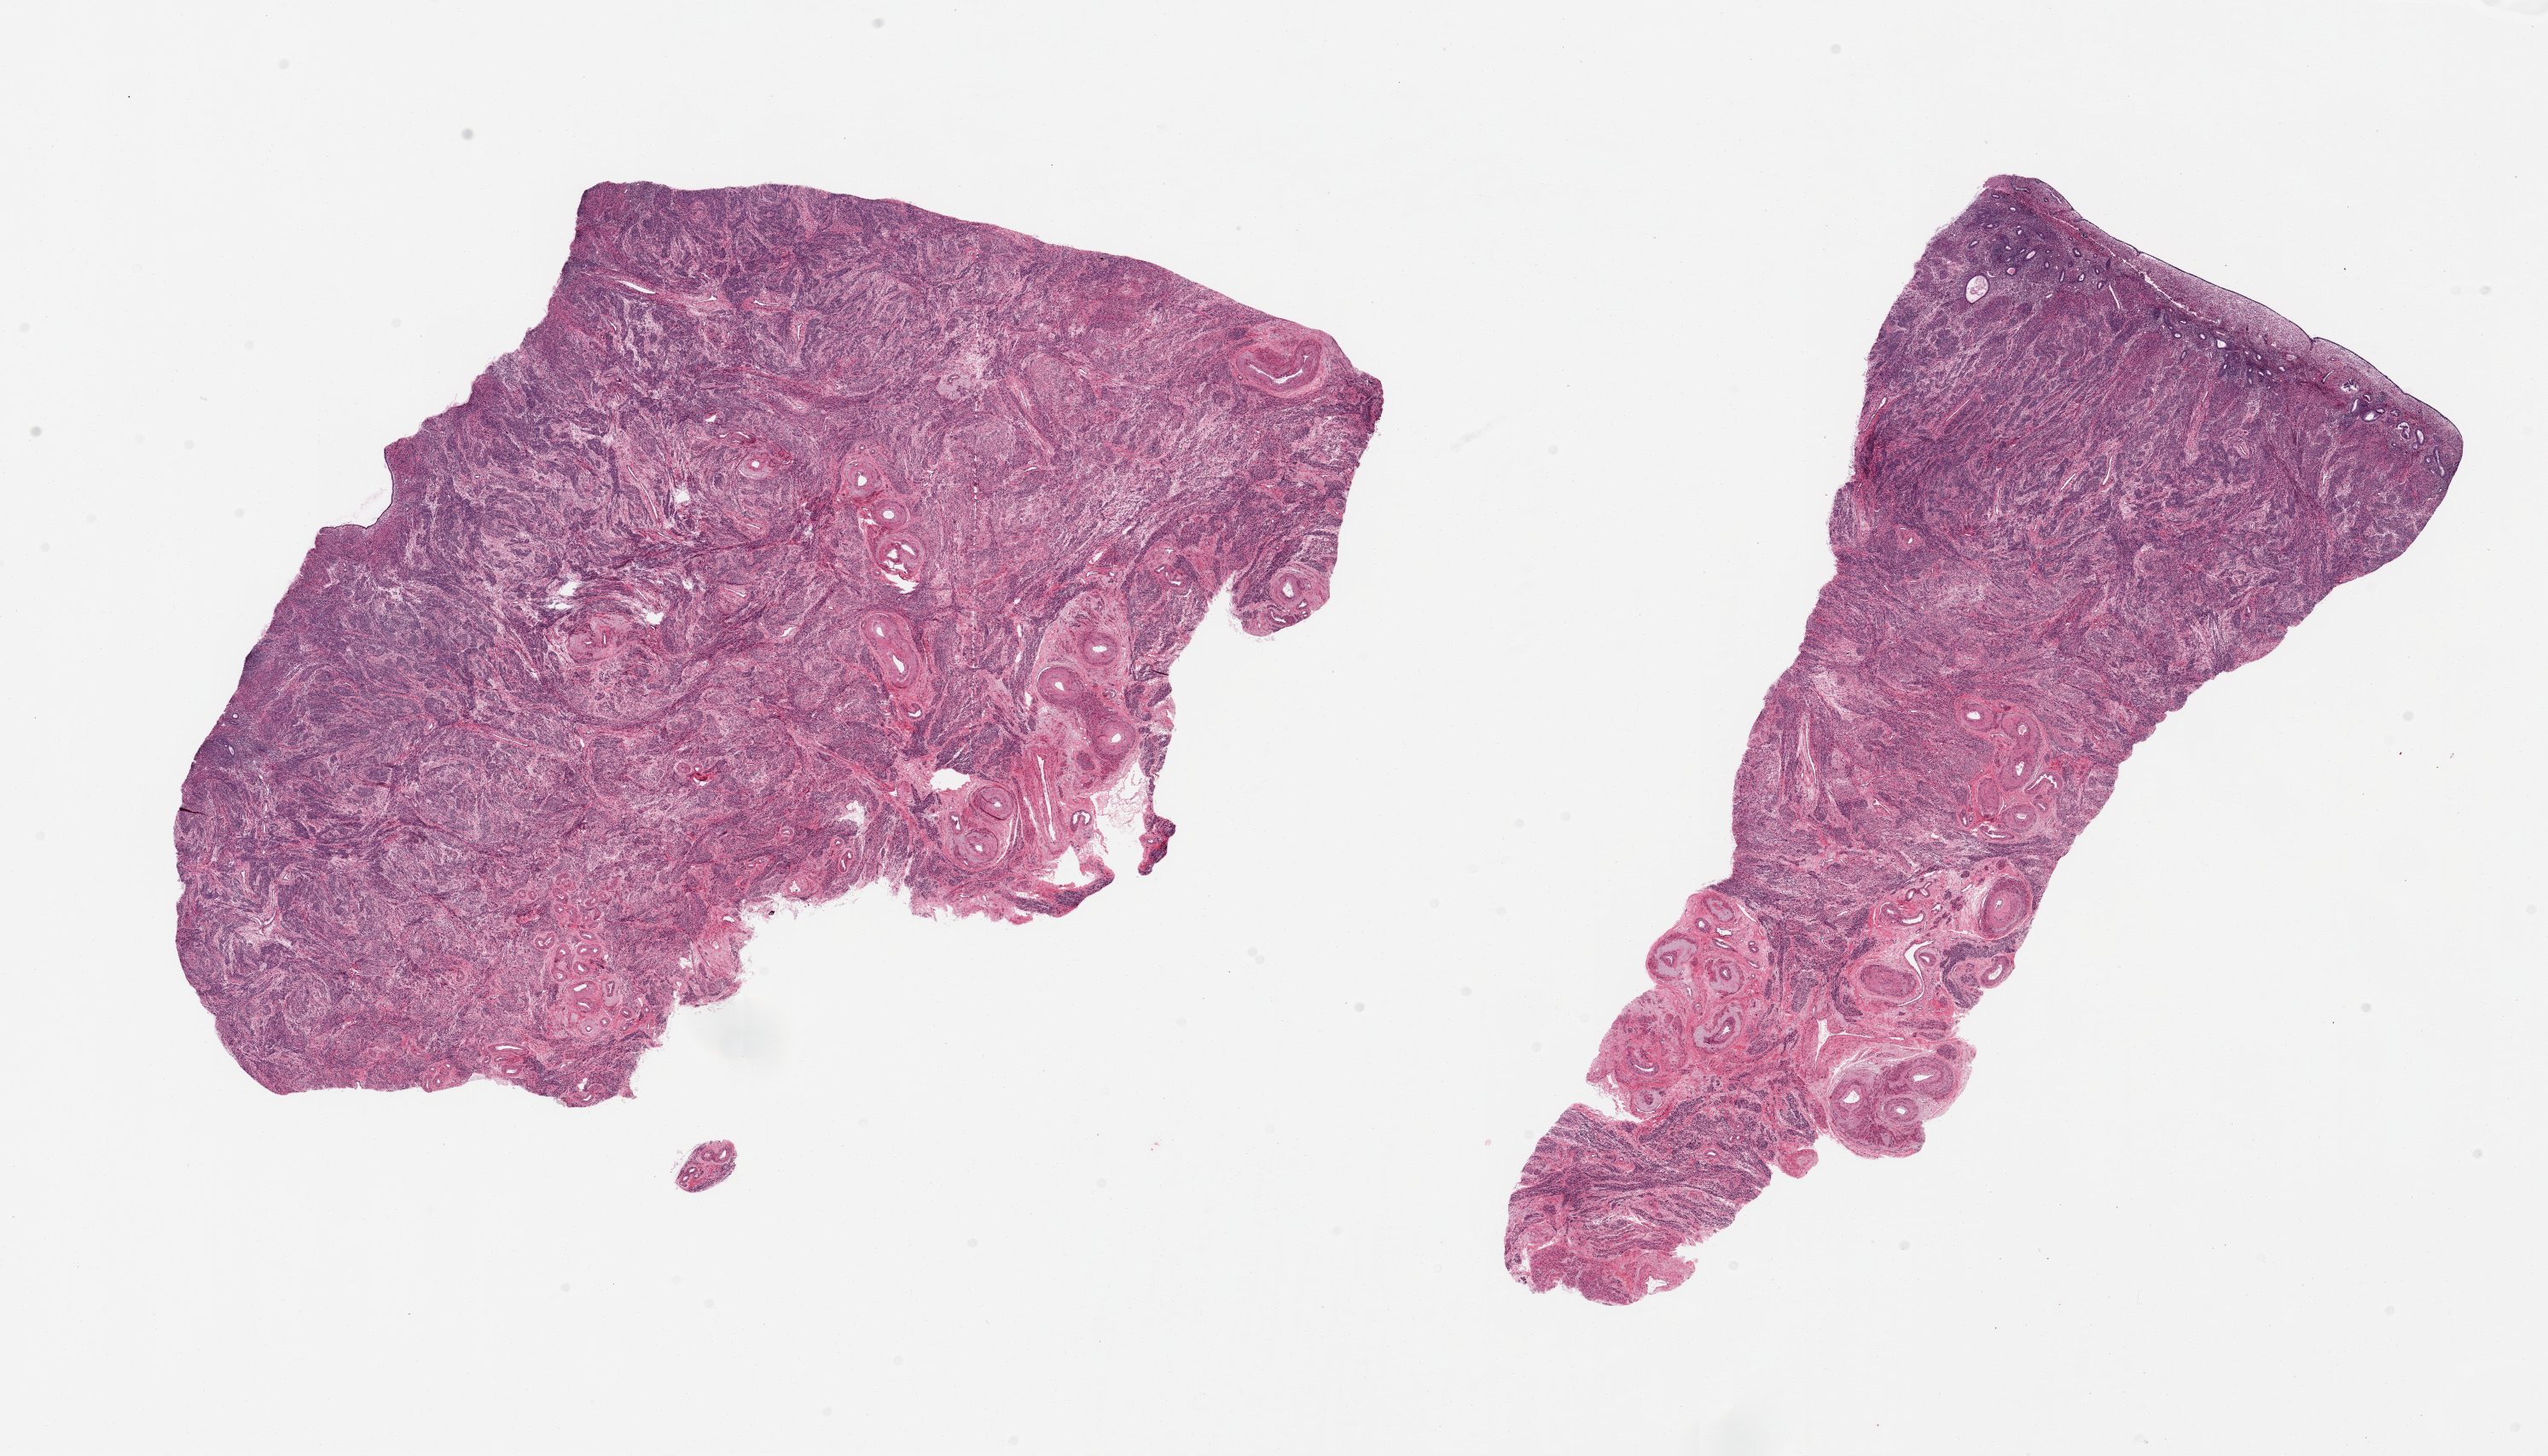
Digitized hematoxylin and eosin (H&E)-stained section, shown as a low-resolution overview of the whole scanned area (about 23.6 x 13.5 mm, from a 20x scan). PAXgene-fixed, paraffin-embedded tissue. Sampled site (target tissue): uterus. Donor tissue sample.
Pathologist's review note for this sample: 2 pieces: 1 with thin atrophic endometrium; other only myometrium (in this cut).